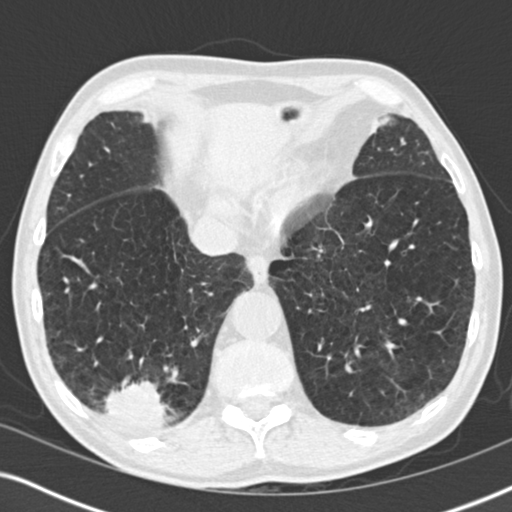
Low-dose screening chest CT, axial slice; baseline screening round; lung window (W 1500 / L -600 HU); 2 mm slice thickness; standard (soft-tissue) reconstruction kernel (B30f); slice 140 of 196 in the series. Male, age 64 years at enrolment.
- Expert-annotated lung lesion, bounding box (x1, y1, x2, y2) in pixels: (81, 367, 179, 449).
- The screening reader recorded 3 non-calcified nodules or masses ≥4 mm on this exam (lingula, lingula, right lower lobe); which of them this box marks is not recorded.
- Official screen result: positive, change unspecified: nodule(s) >= 4 mm or enlarging nodule(s), mass(es), or other non-specific abnormalities suspicious for lung cancer.